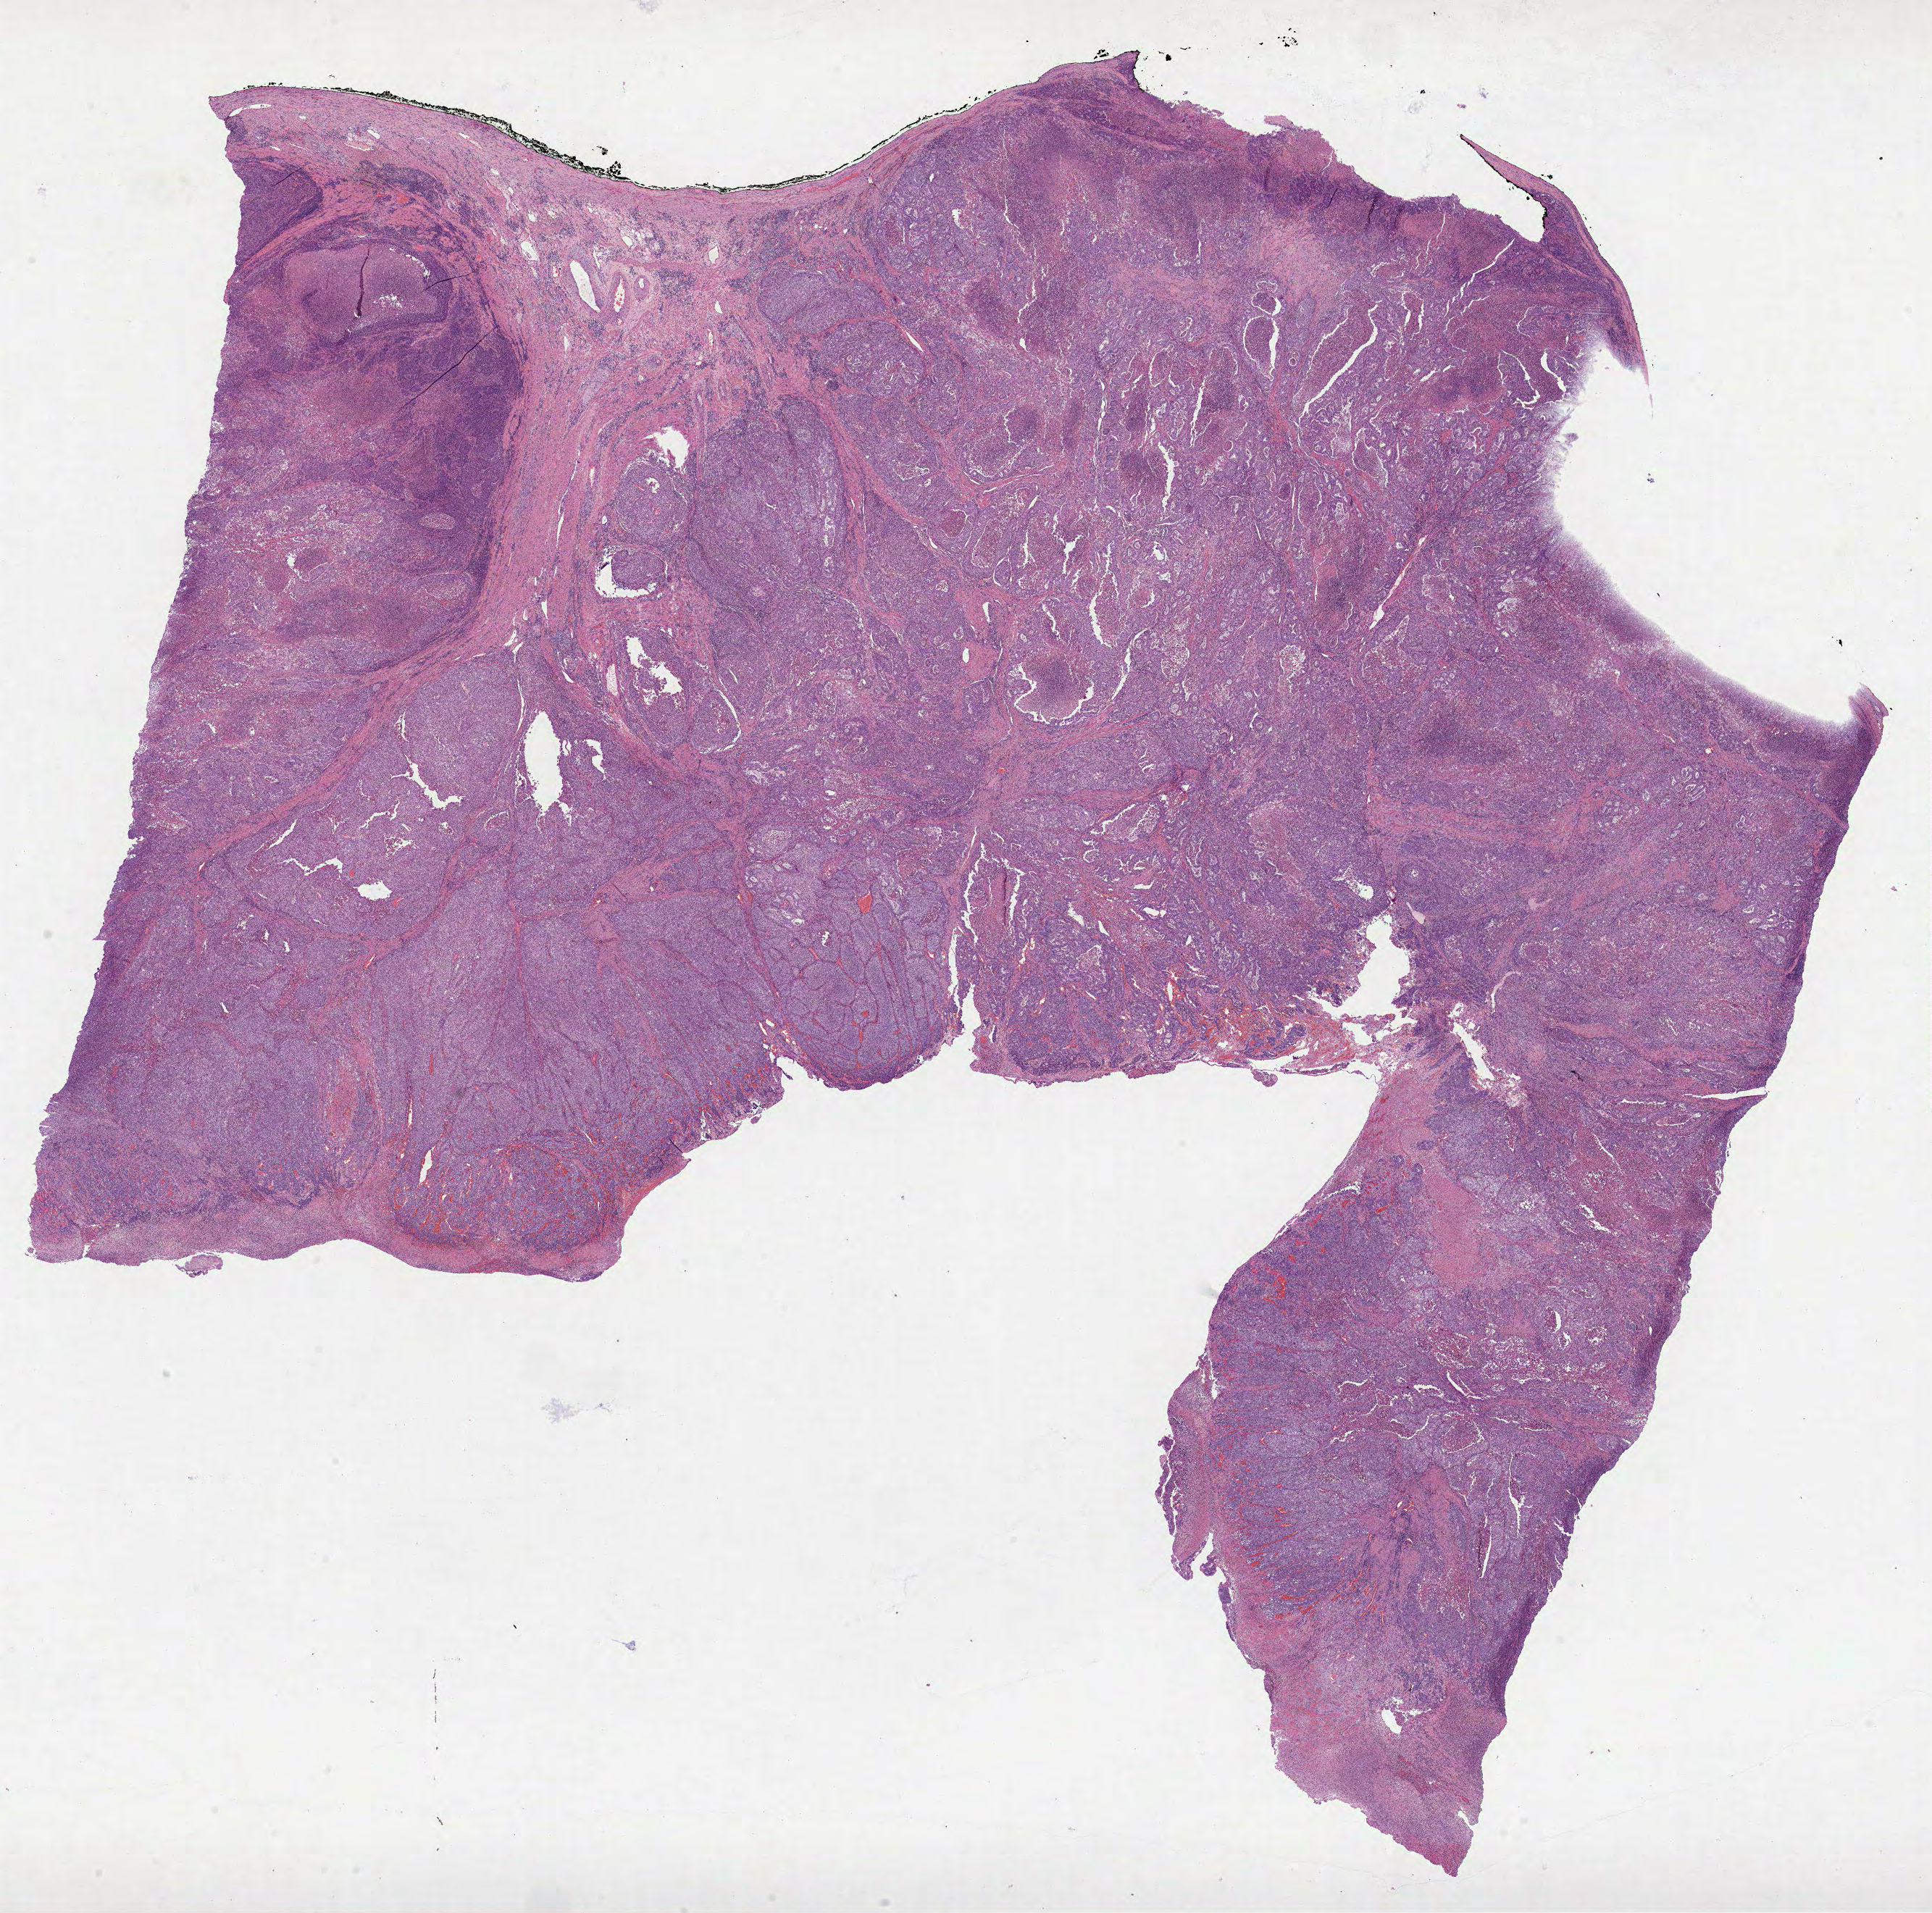
Whole-slide histology image, Hematoxylin and eosin (H&E) stained, whole scanned area (about 21.5 x 21.3 mm) shown as a low-resolution overview, FFPE section, sample: primary tumour, stomach. Patient: male, age at initial diagnosis 55 years. Histologic grade: G3 (poorly differentiated).
AJCC pathologic stage: IIA. Histologic diagnosis: Adenocarcinoma, NOS (fundus of stomach). Lymph nodes positive (case pathology): 0 of 27 examined.